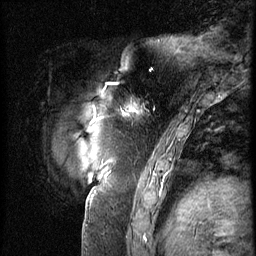
Breast MRI (dynamic contrast-enhanced), one sagittal slice. Position 12 of 62 along the scan axis. 3 images stored at this slice position (order not interpretable as contrast timing). 1.5 T. TE 4.2 ms, TR 9 ms. 2.5 mm slice thickness. 256 × 256 image matrix, field of view 180 × 180 mm. Female patient, age 57 years. From the clinical record (not read from this slice): setting: breast cancer imaged before/during neoadjuvant chemotherapy; receptor status: triple-negative.
Structures marked on this image (semi-automatic segmentation, software-assisted and operator-edited):
- analysis volume of interest (the breast-tissue region the enhancement analysis was run in; not a lesion): bounding box <105,84,158,135> (left, top, right, bottom; pixels)
- tumour enhancement mask (voxels above the 140 % enhancement threshold inside the analysis volume of interest): <105,86,139,115>